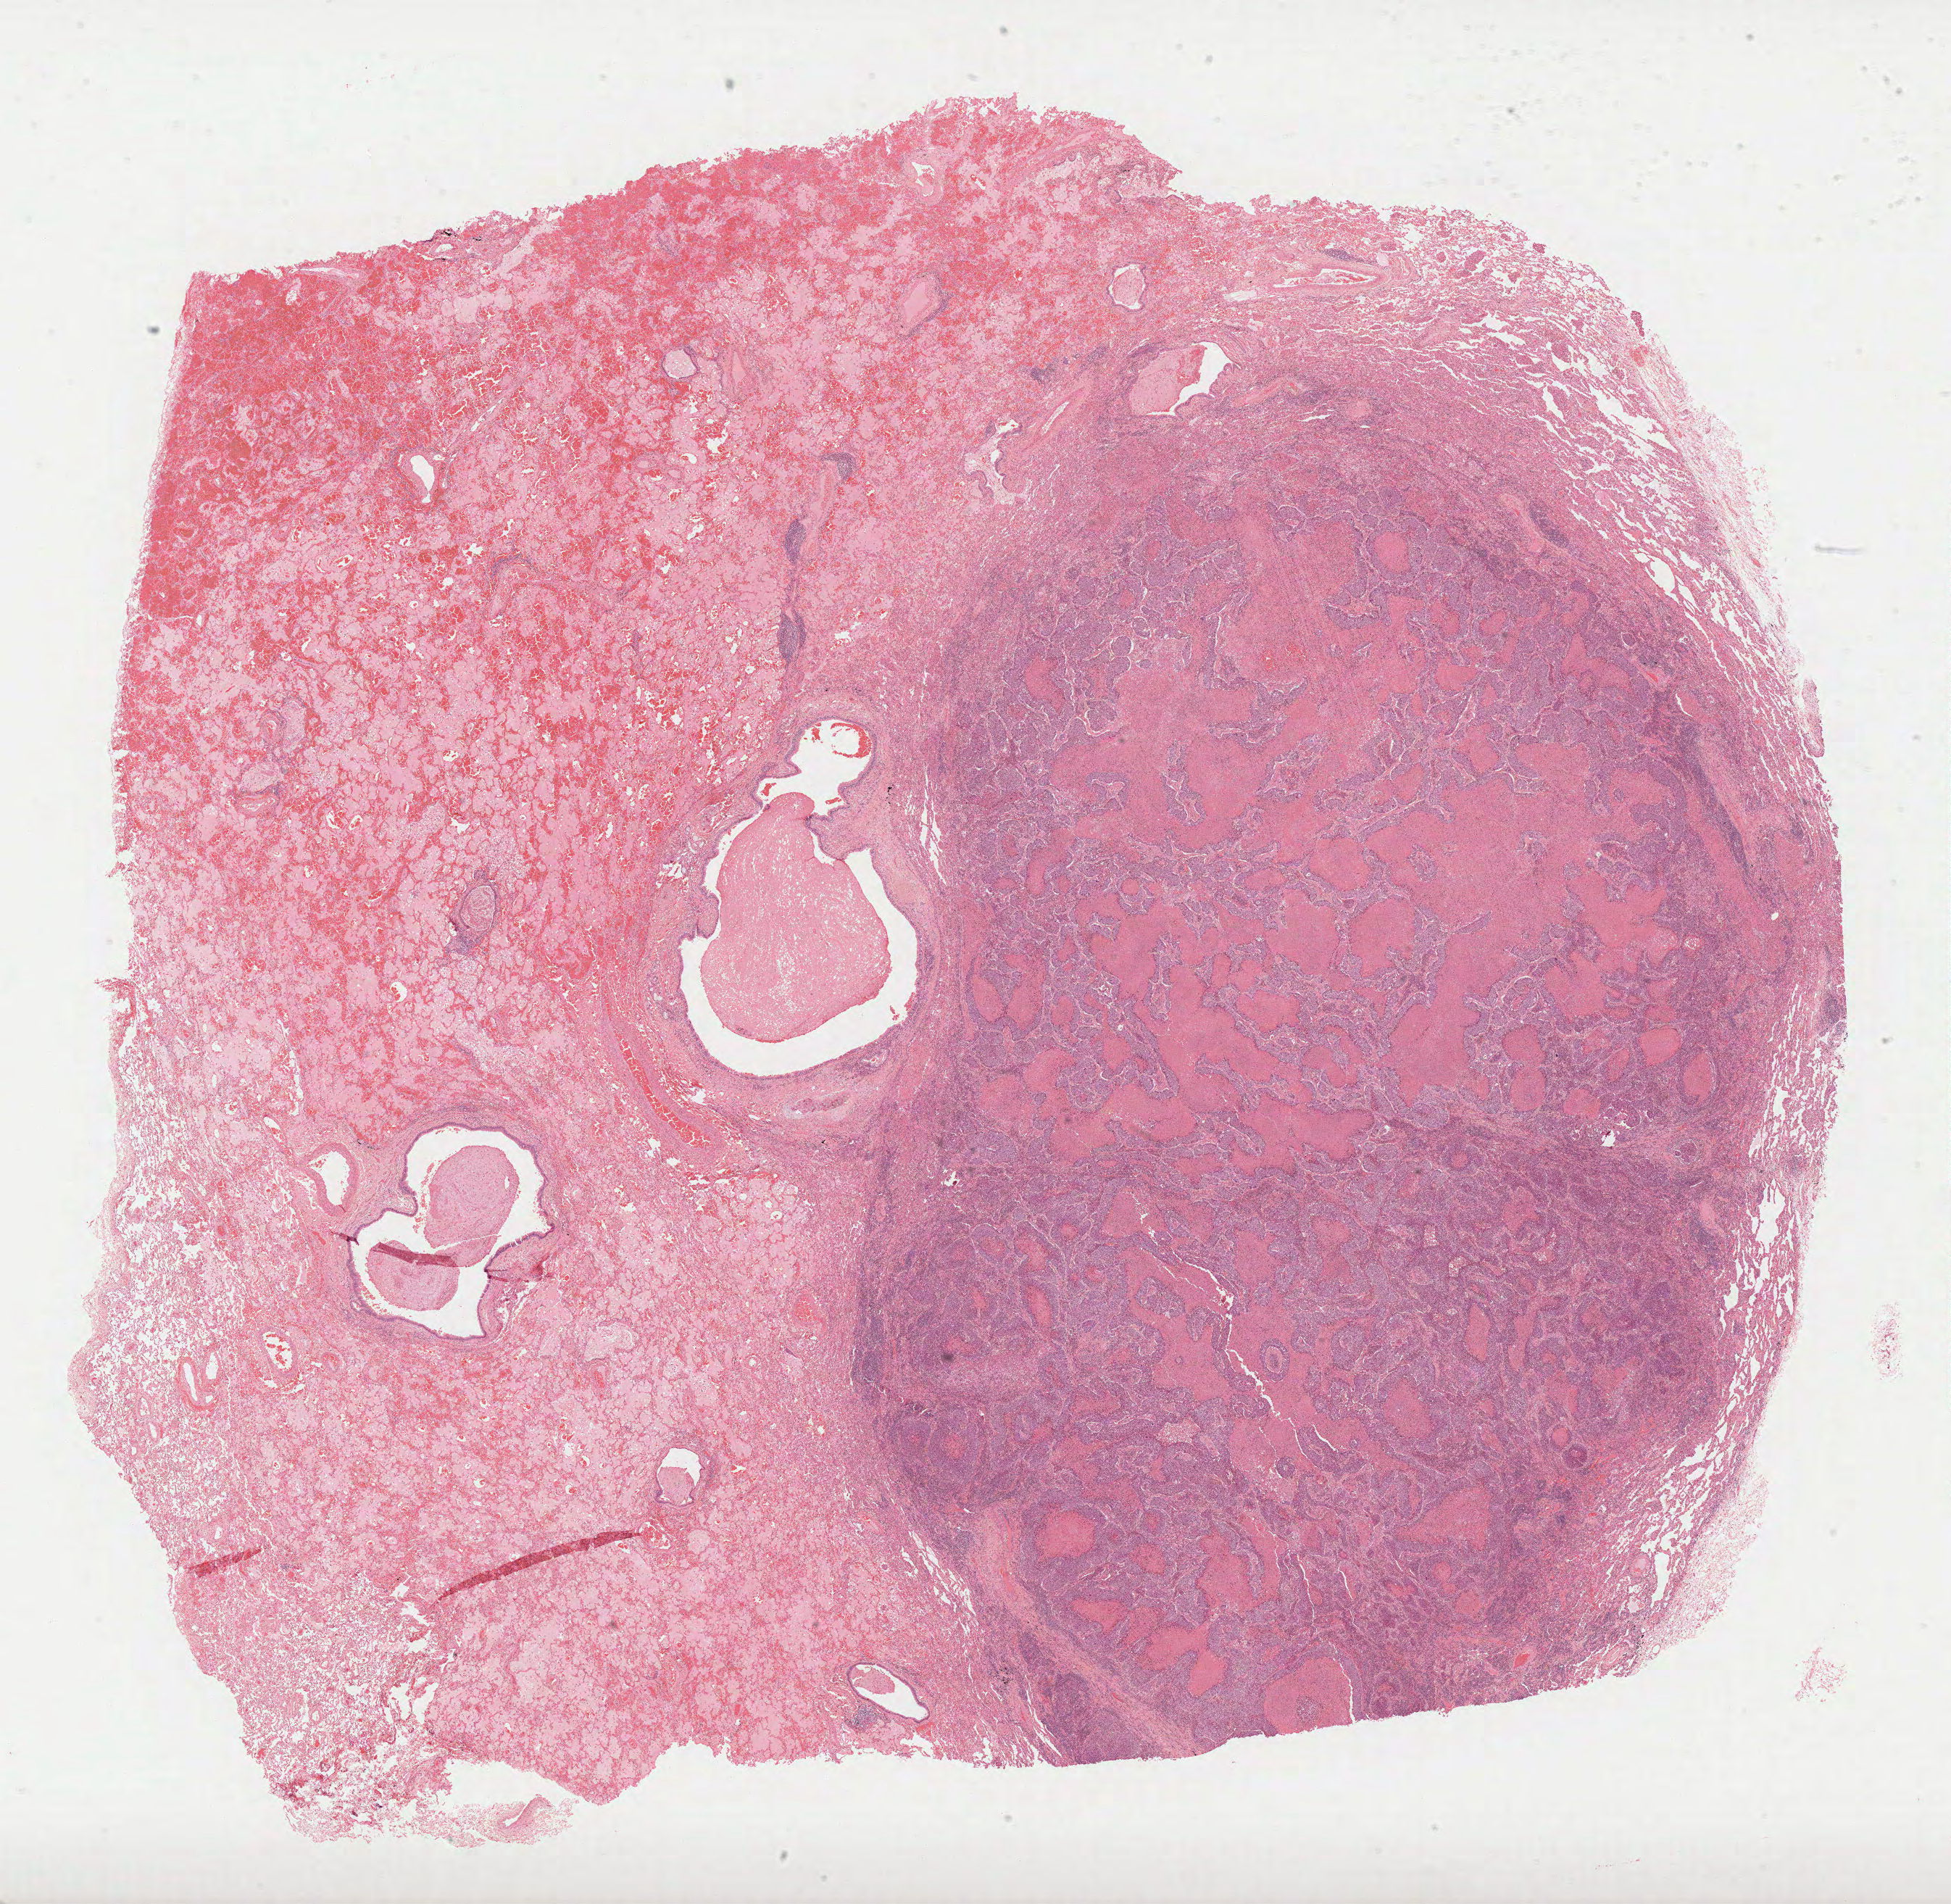
H&E whole-slide image — shown as a low-resolution overview of the whole scanned area (about 21.7 x 21.2 mm); formalin-fixed paraffin-embedded (FFPE) diagnostic section; lung, primary tumour sample. Male, age 63 years at initial diagnosis.
AJCC pathologic stage: IIB. Laterality: left. Pathologic diagnosis: Squamous cell carcinoma, NOS (lower lobe, lung).